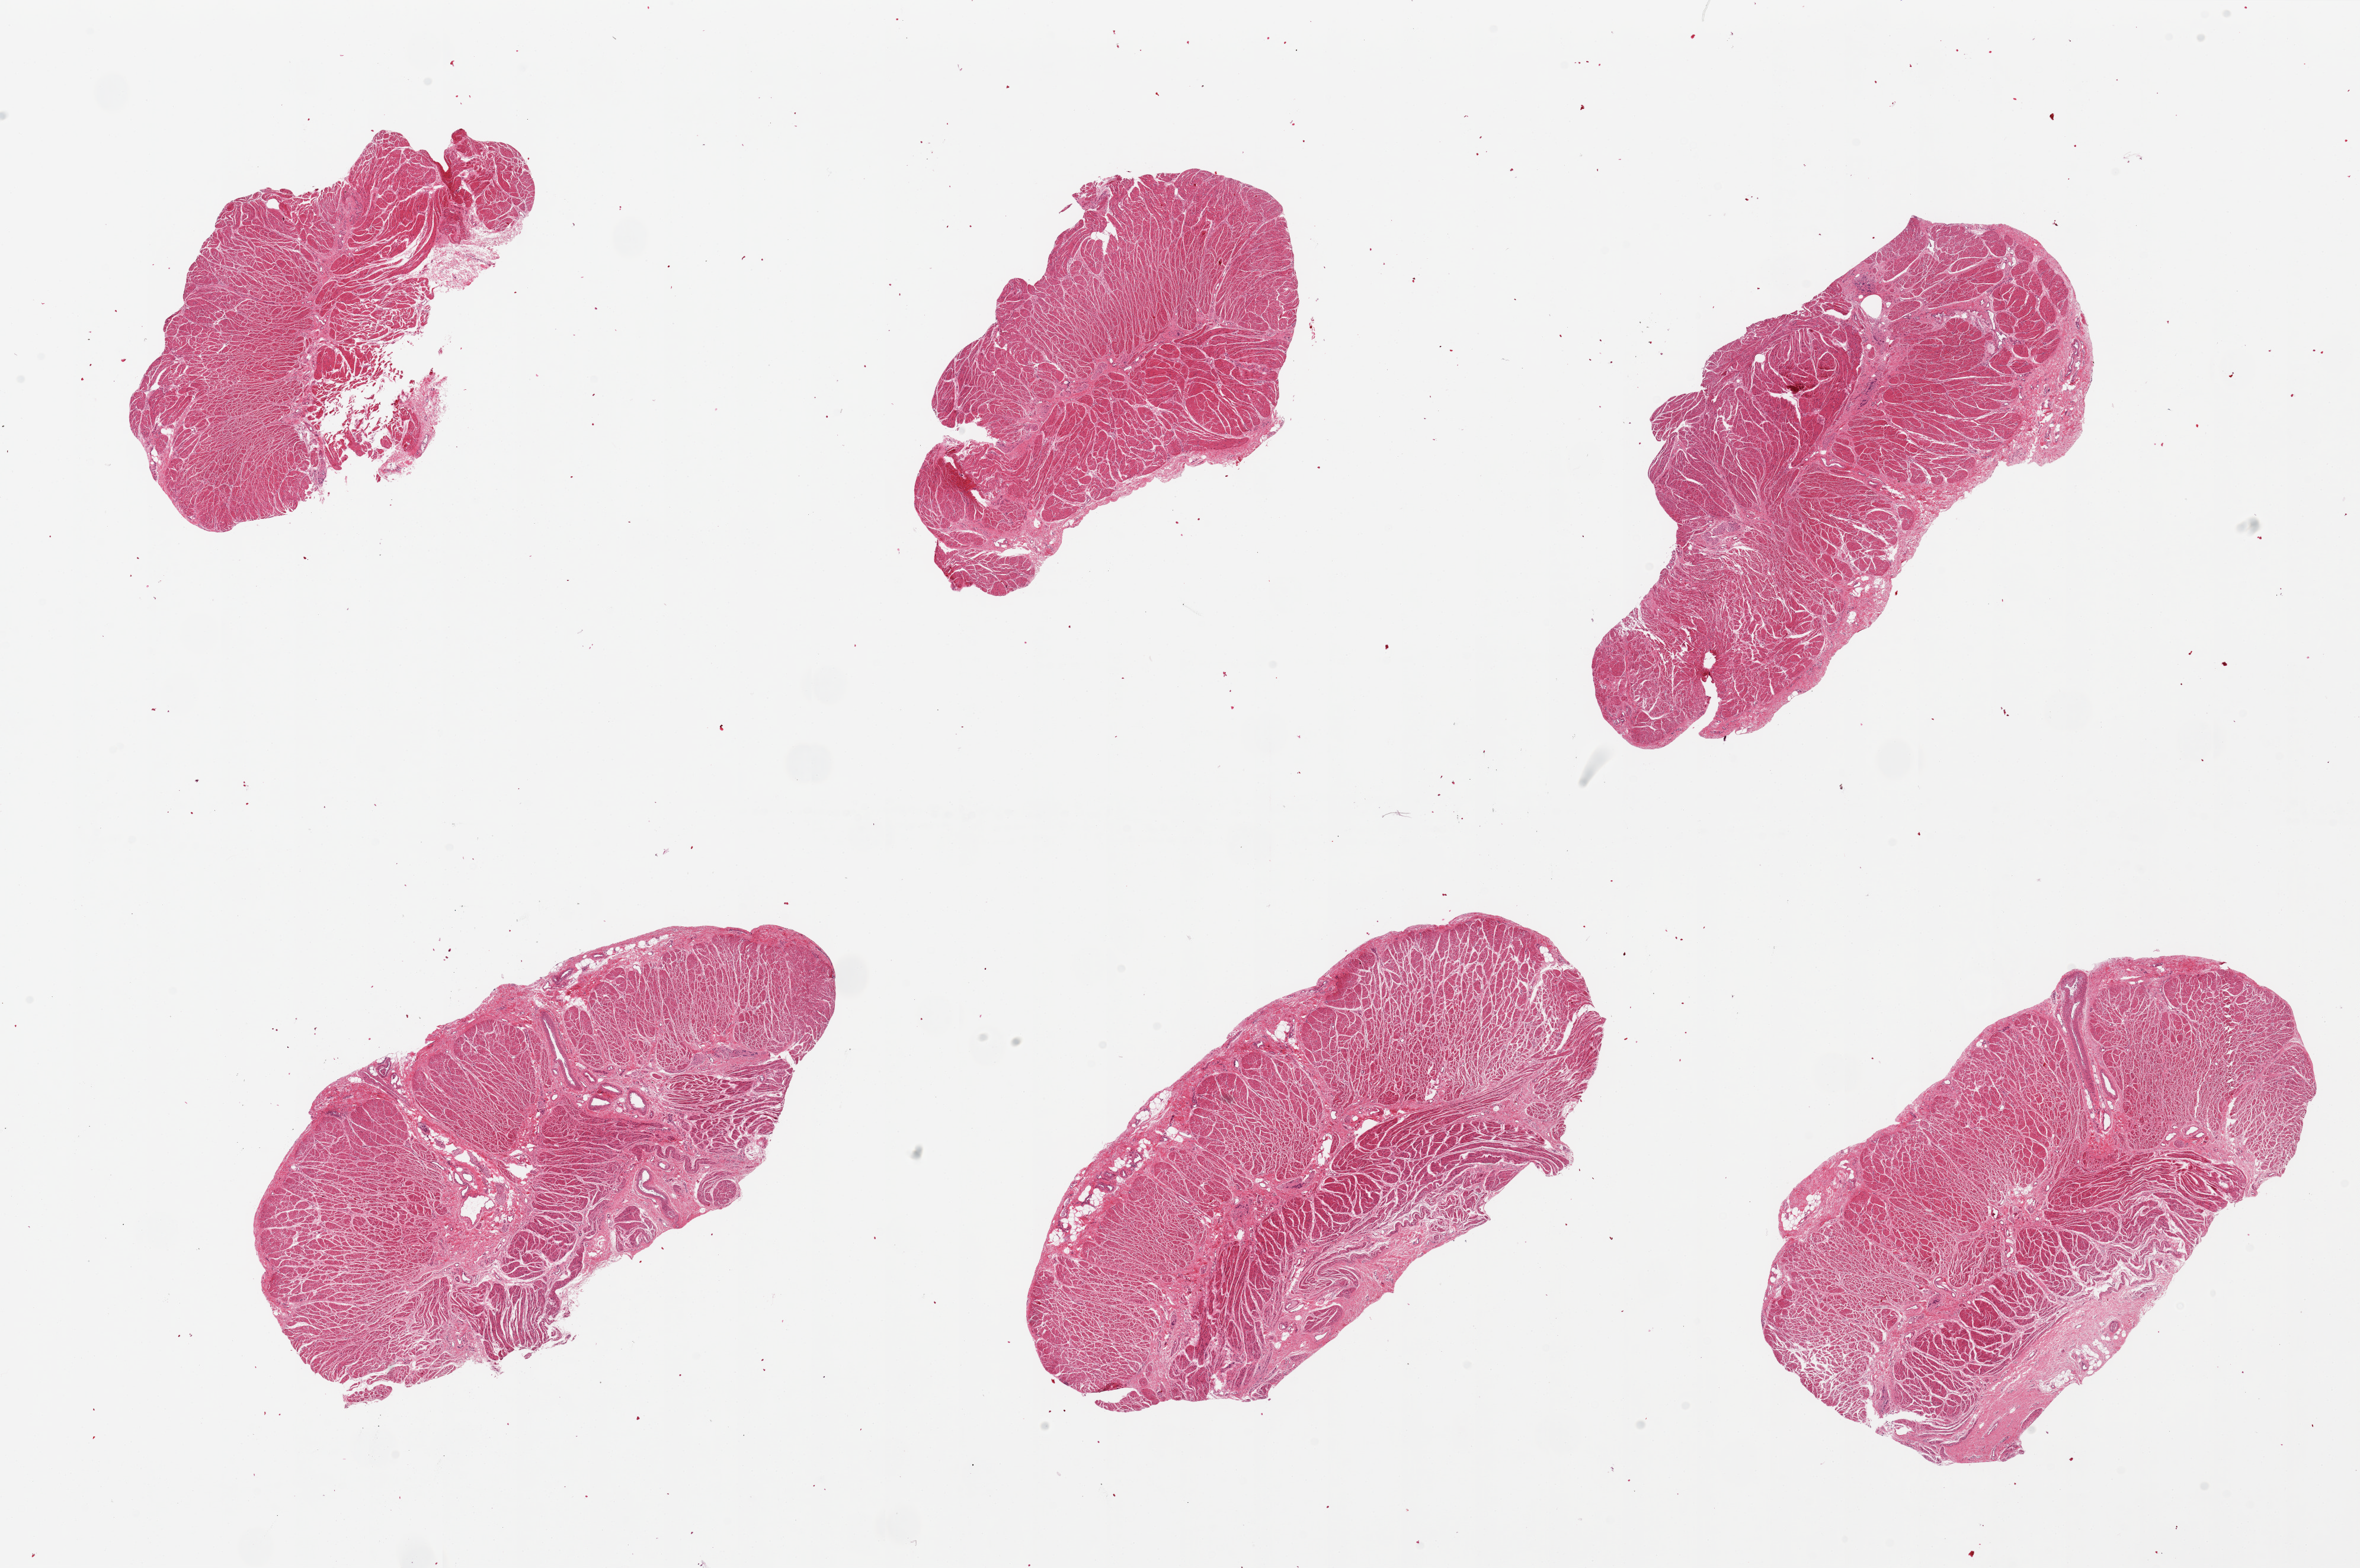
Whole-slide image, hematoxylin and eosin (H&E) stain — low-resolution overview of the scanned area, about 31.5 x 20.9 mm, PAXgene-fixed, paraffin-embedded tissue, target tissue: gastroesophageal junction, donor tissue sample. Donor: male.
Reviewer comment on this tissue sample: 6 pieces, well trimmed.